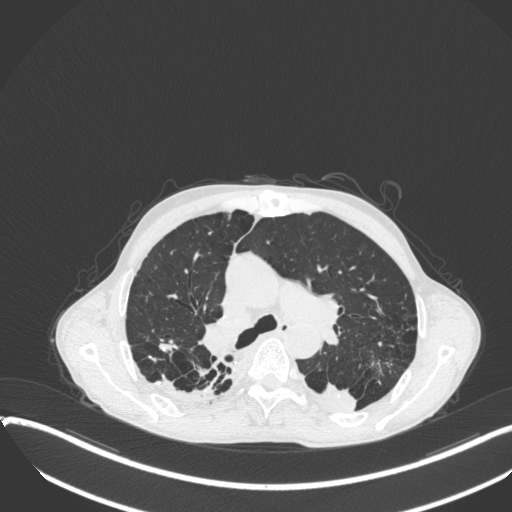
Chest CT, one axial slice; slice 255 of 400 in the series (ordered by position); 120 kVp; lung window (W 1500 / L -600 HU); 1 mm slice thickness; 512 × 512 image matrix, field of view 400 × 400 mm. Male patient, age 57 years. From the clinical record (not read from this slice): clinical TNM (as recorded): T4 N0 M0.
Outlined on this slice (bounding box drawn by a radiologist):
- lung tumour (recorded histology: squamous cell carcinoma): box from (x=308, y=377) to (x=359, y=418) px